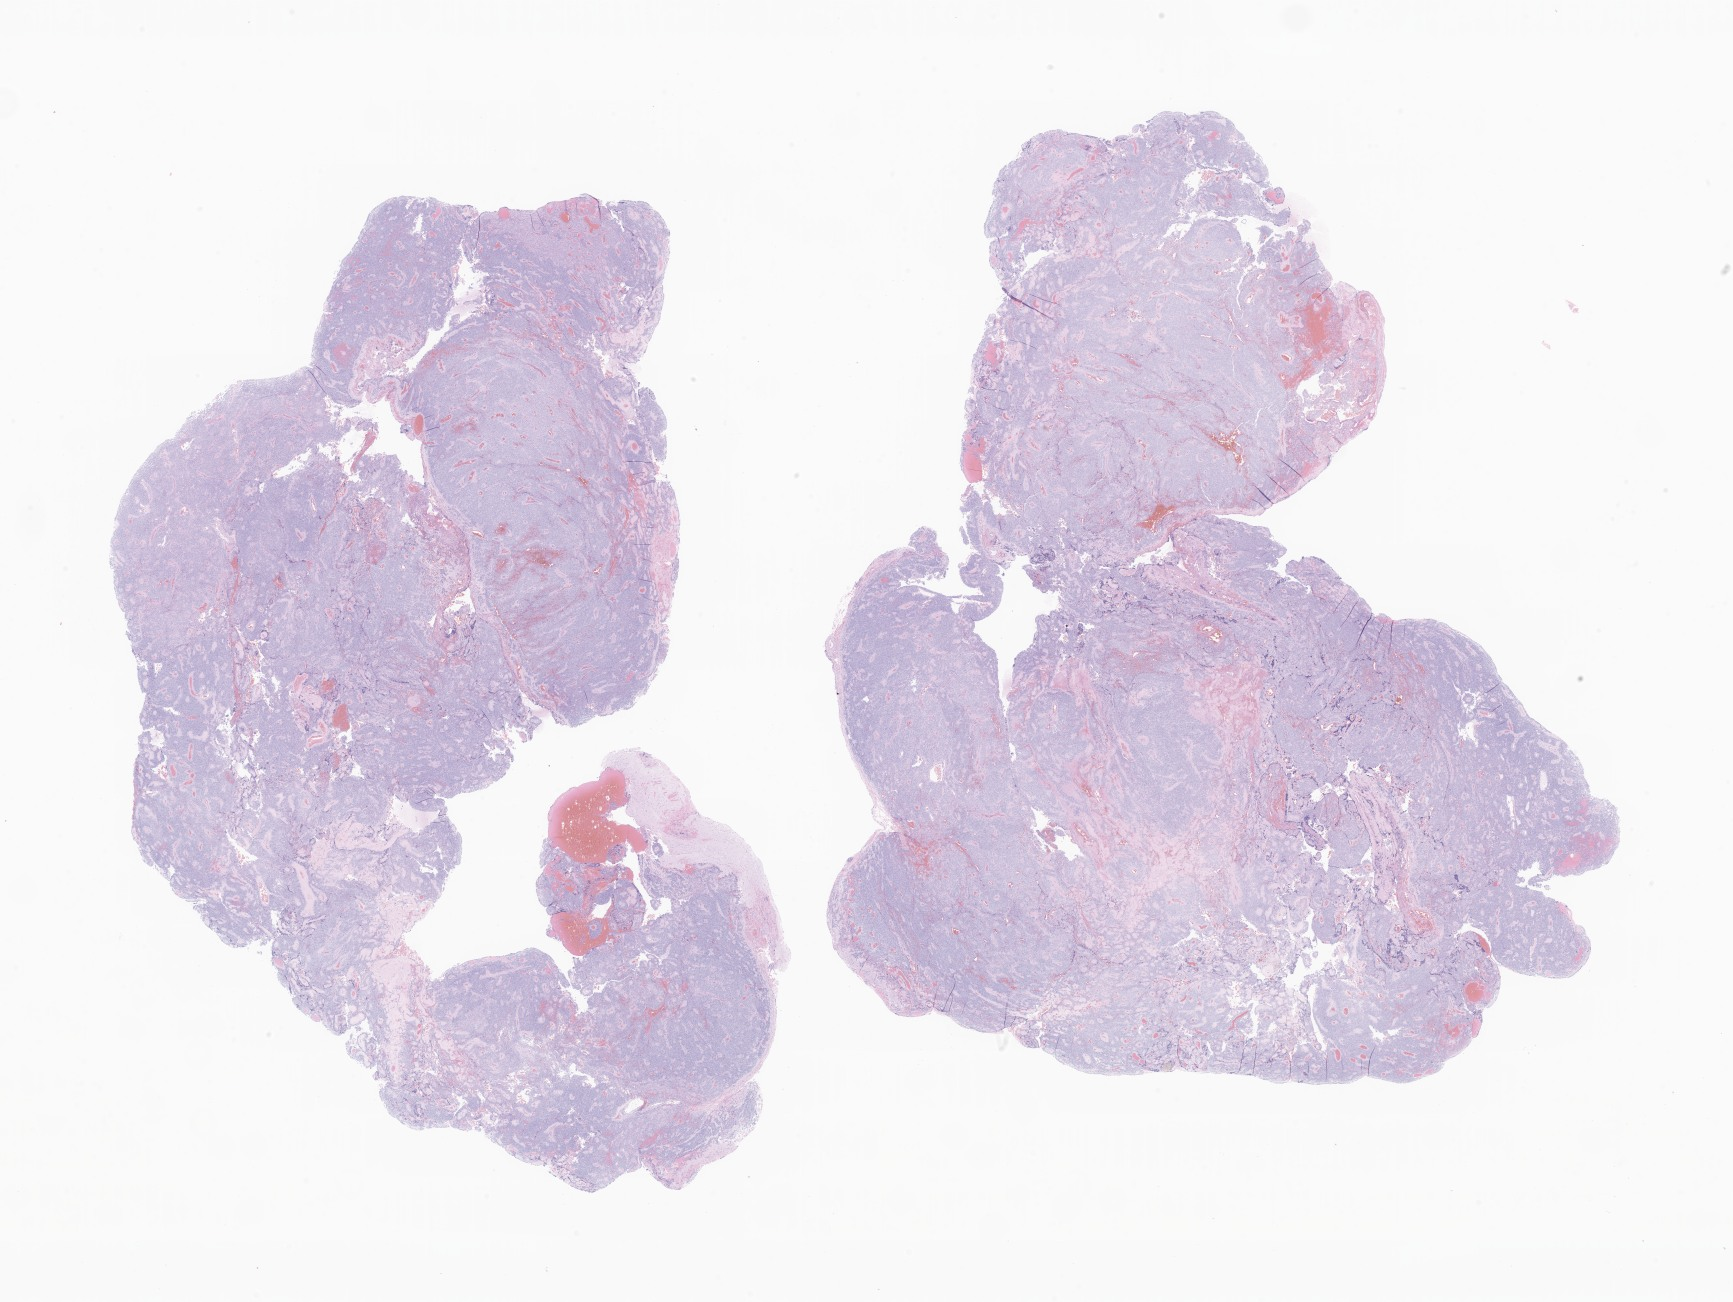
Whole-slide image, hematoxylin and eosin (H&E) stain of tumor tissue from the brain, shown as a low-resolution overview of the whole scanned area (about 29.2 x 22.0 mm); FFPE section. Male patient, age 109 months (9 years 1 month).
Recorded diagnosis: Neoplasm, uncertain whether benign or malignant.